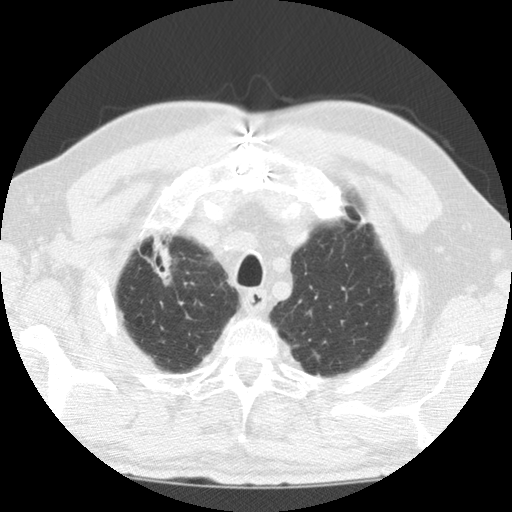
Axial slice from a low-dose chest CT screening exam. First (baseline) screen. Lung window (W 1500 / L -600 HU). Standard (soft-tissue) reconstruction kernel (STANDARD). 120 kVp. 512 × 512 image matrix, field of view 320 × 320 mm. Male, age 69 years at enrolment. Former smoker at enrolment.
- Lesion marked by an expert reader, box from (x=106, y=217) to (x=184, y=296) px.
- Screening reader's record for this exam: no non-calcified nodule ≥4 mm recorded.
- Official screen result: negative screen, minor abnormalities not suspicious for lung cancer.
- Later outcome: lung cancer diagnosed 171 days after this screen — adenocarcinoma, NOS, right upper lobe, poorly differentiated (G3), stage IIIB (AJCC 6th edition), 40 mm at pathology.